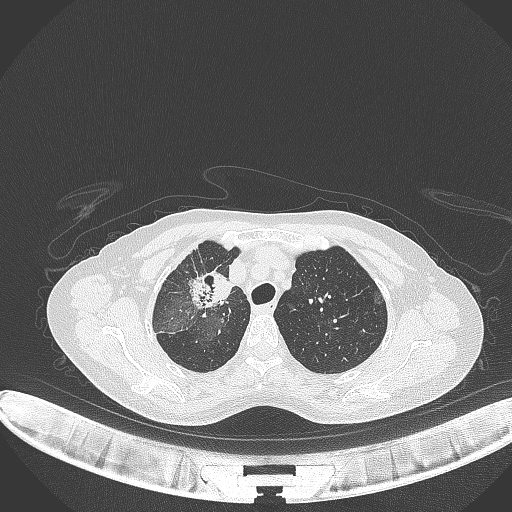
Chest CT, one axial slice. Position 255 of 284 along the scan axis. Lung window (W 1500 / L -600 HU). 512 × 512 image matrix, field of view 400 × 400 mm. Female patient, age 59 years. From the clinical record (not read from this slice): clinical TNM (as recorded): T3 N0 M0; histopathological grade: G1.
Annotated regions visible in this slice (bounding box drawn by a radiologist):
- lung tumour (recorded histology: adenocarcinoma): box from (x=188, y=268) to (x=236, y=314) px